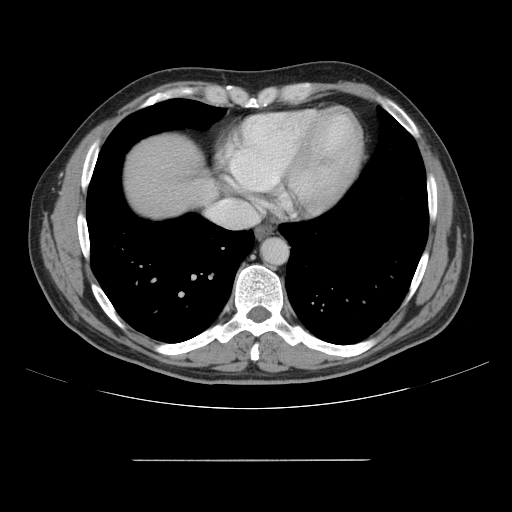
Contrast-enhanced abdominal CT, one axial slice. Slice 146 of 164 in the series (ordered by position). Intravenous contrast given. Soft-tissue window (W 400 / L 40 HU). 2.5 mm slice thickness. 512 × 512 image matrix, field of view 404 × 404 mm. Male patient, age 54 years. Case-level facts recorded for this patient, not image findings: diagnosis: colorectal cancer liver metastases, imaged before liver resection.
Outlined on this slice (expert manual segmentation):
- hepatic veins: box from (x=208, y=199) to (x=258, y=224) px
- liver: (x=125, y=135)–(x=215, y=216)
- planned liver remnant (the part of the liver to remain after resection): (x=125, y=134)–(x=216, y=216)